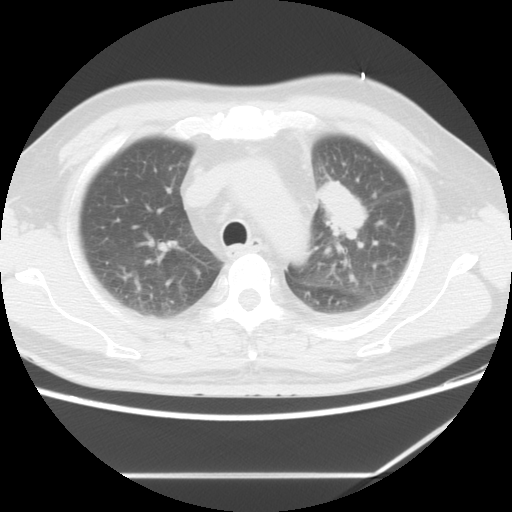
Chest CT, one axial slice. Slice 7 of 13 in the series (ordered by position). Lung window (W 1500 / L -600 HU). 5 mm slice thickness. 512 × 512 image matrix, field of view 350 × 350 mm. Male patient, age 56 years. From the clinical record (not read from this slice): clinical TNM (as recorded): T2 N3 M1.
Annotated regions visible in this slice (rectangle marked by the reading radiologist):
- lung tumour (recorded histology: adenocarcinoma): box from (x=318, y=177) to (x=373, y=255) px